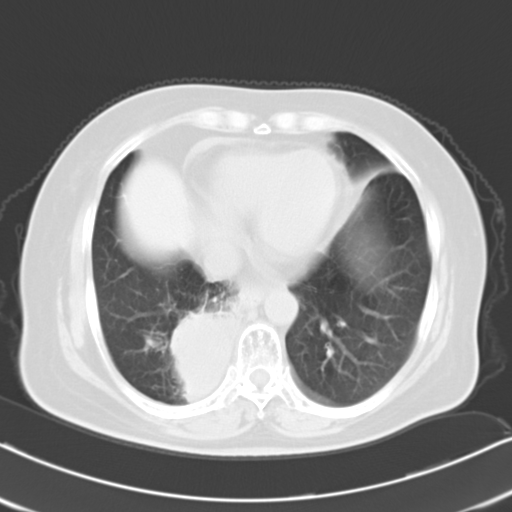
Chest CT, one axial slice; slice 6 of 21 in the series (ordered by position); 120 kVp; lung window (W 1500 / L -600 HU); 10 mm slice thickness; 512 × 512 image matrix, field of view 326 × 326 mm. Female patient, age 61 years. From the clinical record (not read from this slice): clinical TNM (as recorded): T1b N0 M1b.
Annotated regions visible in this slice (rectangle marked by the reading radiologist):
- lung tumour (recorded histology: squamous cell carcinoma): bounding box (x1, y1, x2, y2) in pixels: (163, 310, 242, 405)